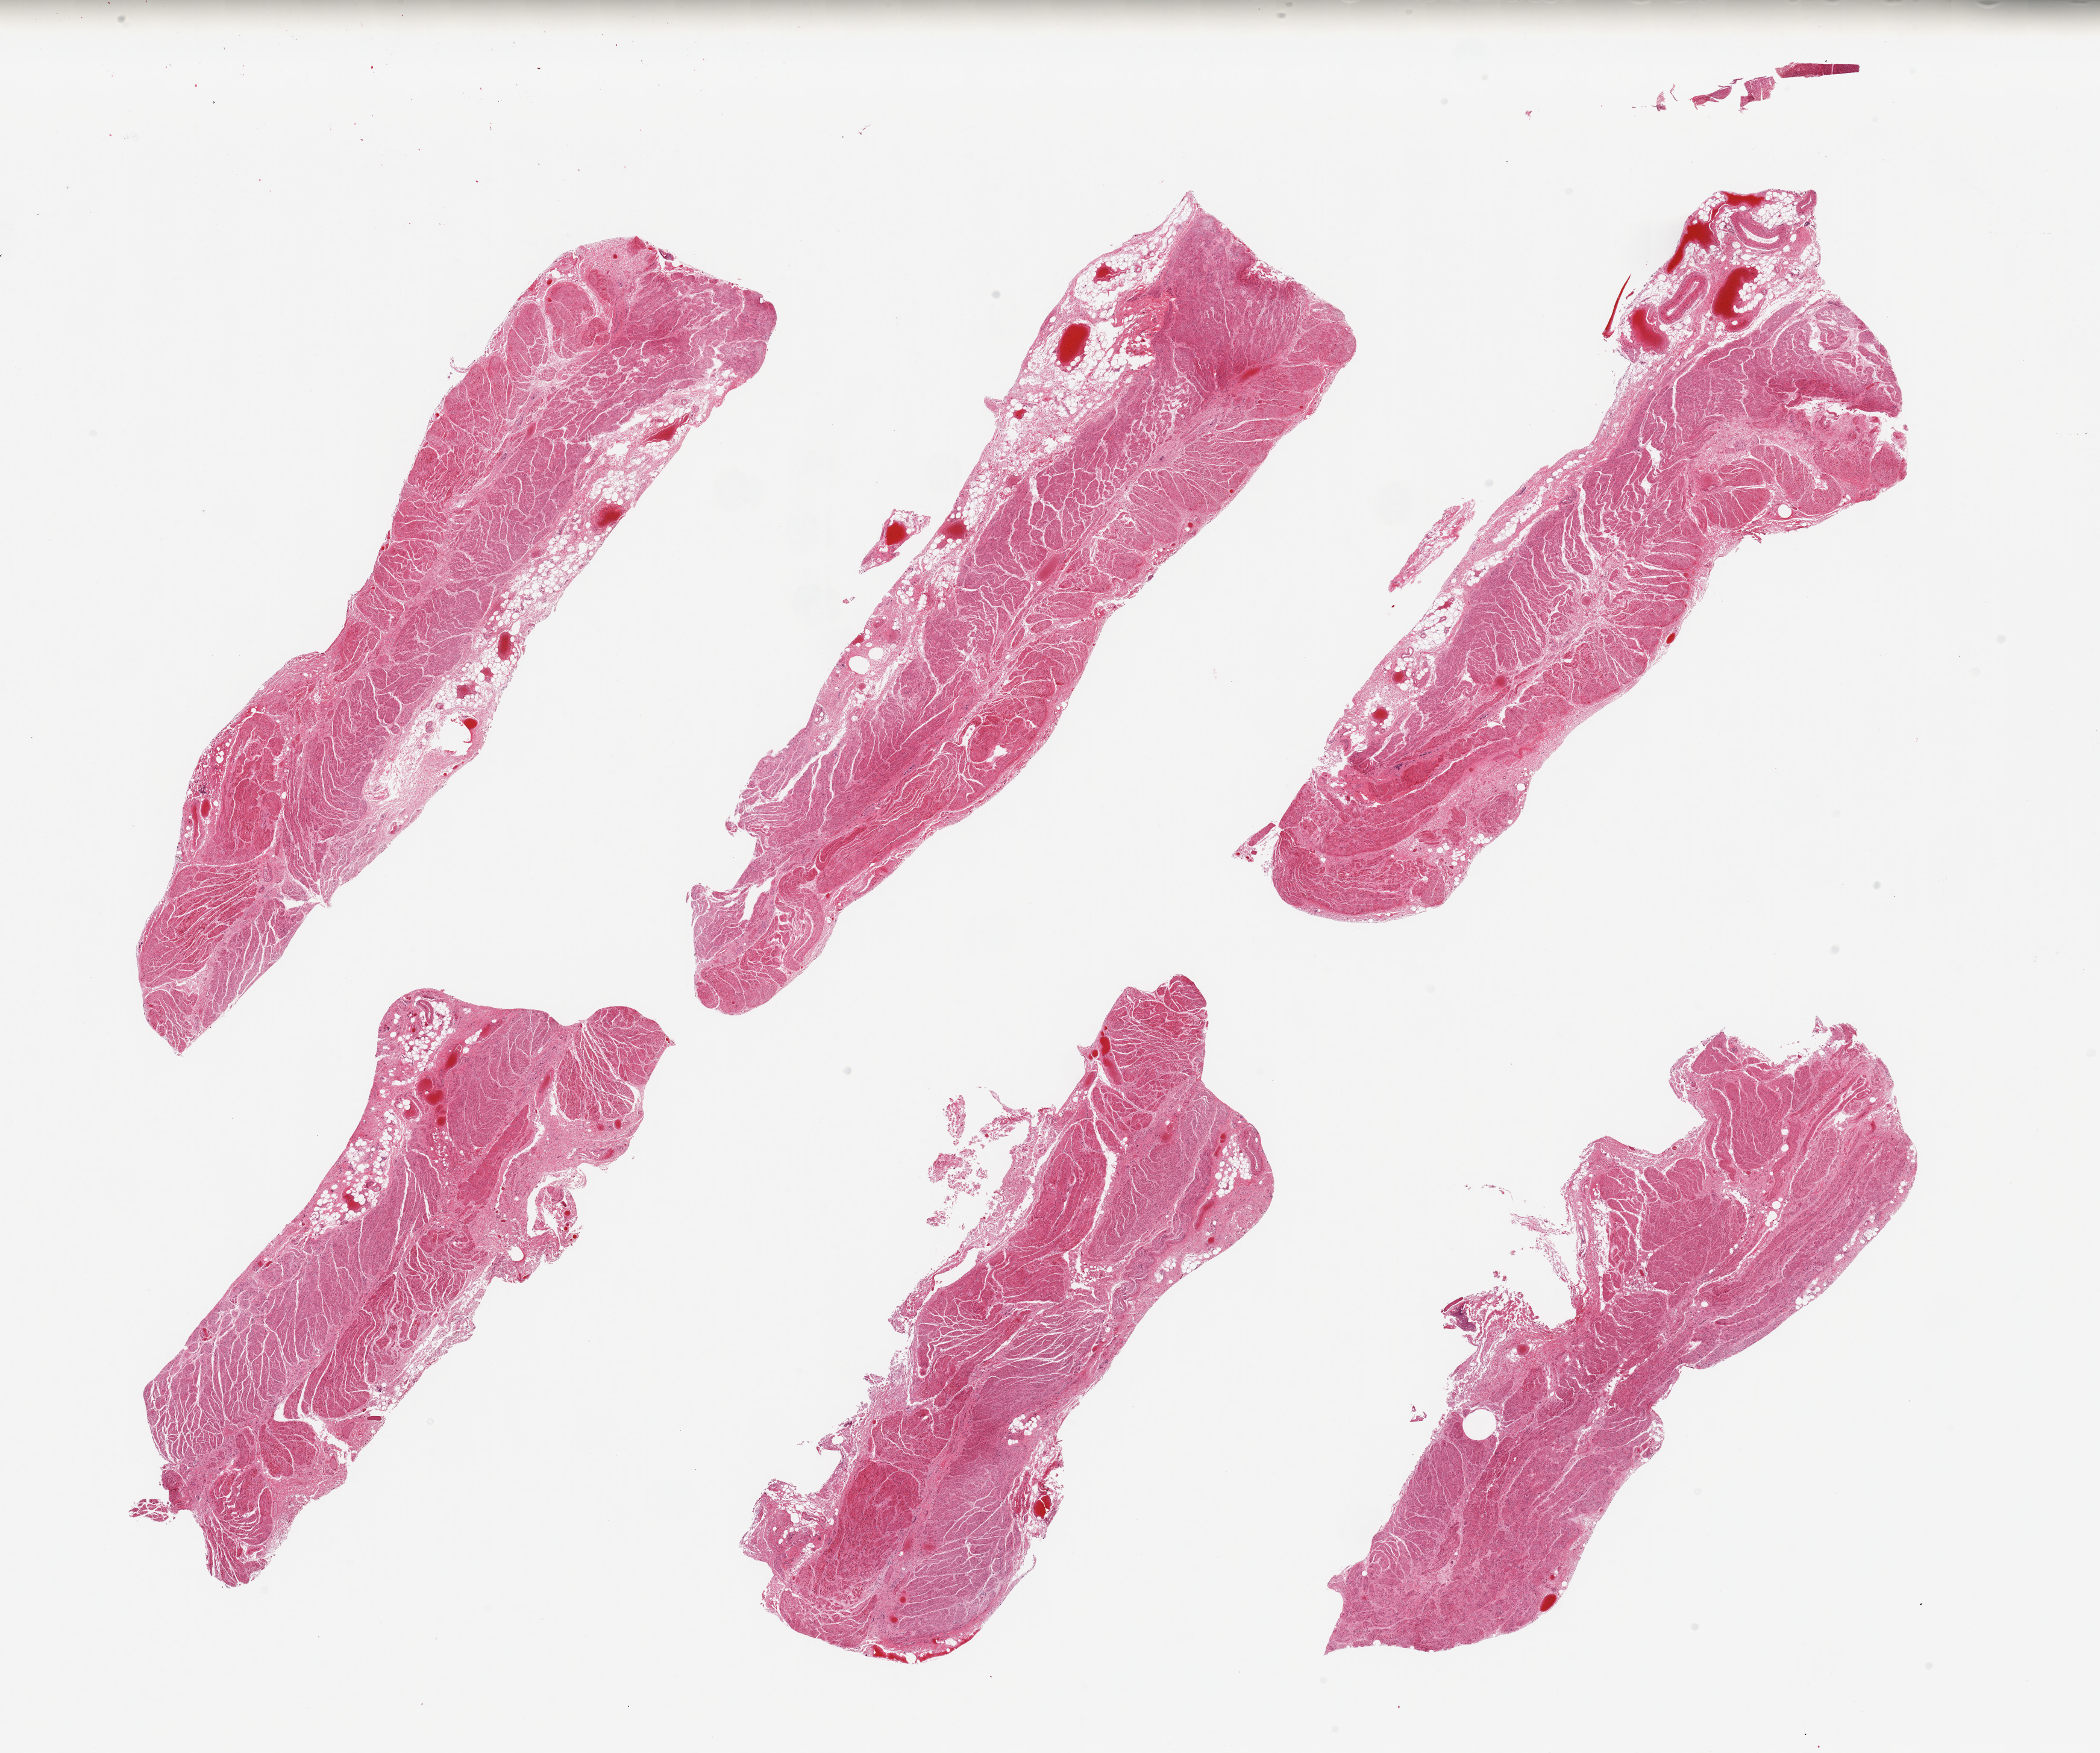
H&E whole-slide image — whole scanned area (about 27.6 x 23.0 mm, slide scanned at 20x) shown as a low-resolution overview; PAXgene-fixed, paraffin-embedded tissue; sampled site (target tissue): gastroesophageal junction; tissue donor sample. Donor: male.
Pathologist's review note for this sample: 6 pieces, confirmed target muscularis; adherent nubbins adipose/vascular elements, up to ~1.5mm.